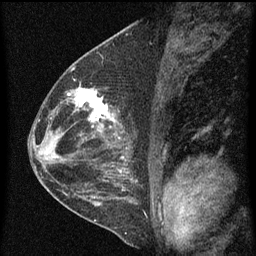
Breast MRI (dynamic contrast-enhanced), one sagittal slice; slice 30 of 60 in the series (ordered by position); dynamic contrast-enhanced series, image 2 of 4 at this slice position (ordered by acquisition); 1.5 T; TE 4.2 ms, TR 8 ms; 256 × 256 image matrix, field of view 180 × 180 mm. Female patient, age 48 years.
Outlined on this slice (semi-automatic segmentation, software-assisted and operator-edited):
- analysis volume of interest (the breast-tissue region the enhancement analysis was run in; not a lesion): bounding box <73,84,115,139> (left, top, right, bottom; pixels)
- tumour enhancement mask (voxels above the 70 % enhancement threshold inside the analysis volume of interest): <73,88,115,129>